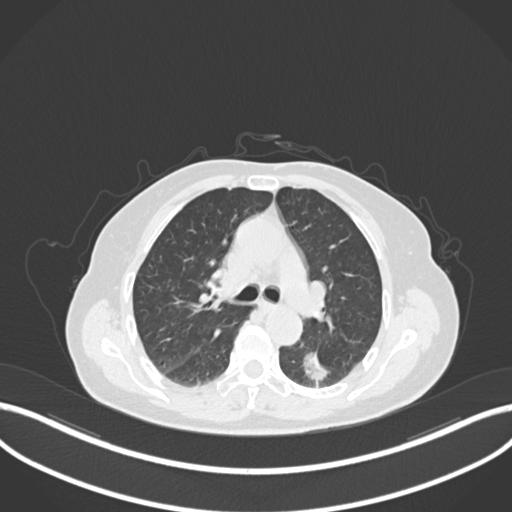
Chest CT, one axial slice. Slice 537 of 727 in the series (ordered by position). Reconstruction kernel B30f. 120 kVp. Lung window (W 1500 / L -600 HU). 512 × 512 image matrix, field of view 400 × 400 mm. Patient: female, 70 years. From the clinical record (not read from this slice): clinical TNM (as recorded): T1c N0 M0.
Structures marked on this image (rectangle marked by the reading radiologist):
- lung tumour (recorded histology: adenocarcinoma): bounding box <299,345,336,383> (left, top, right, bottom; pixels)